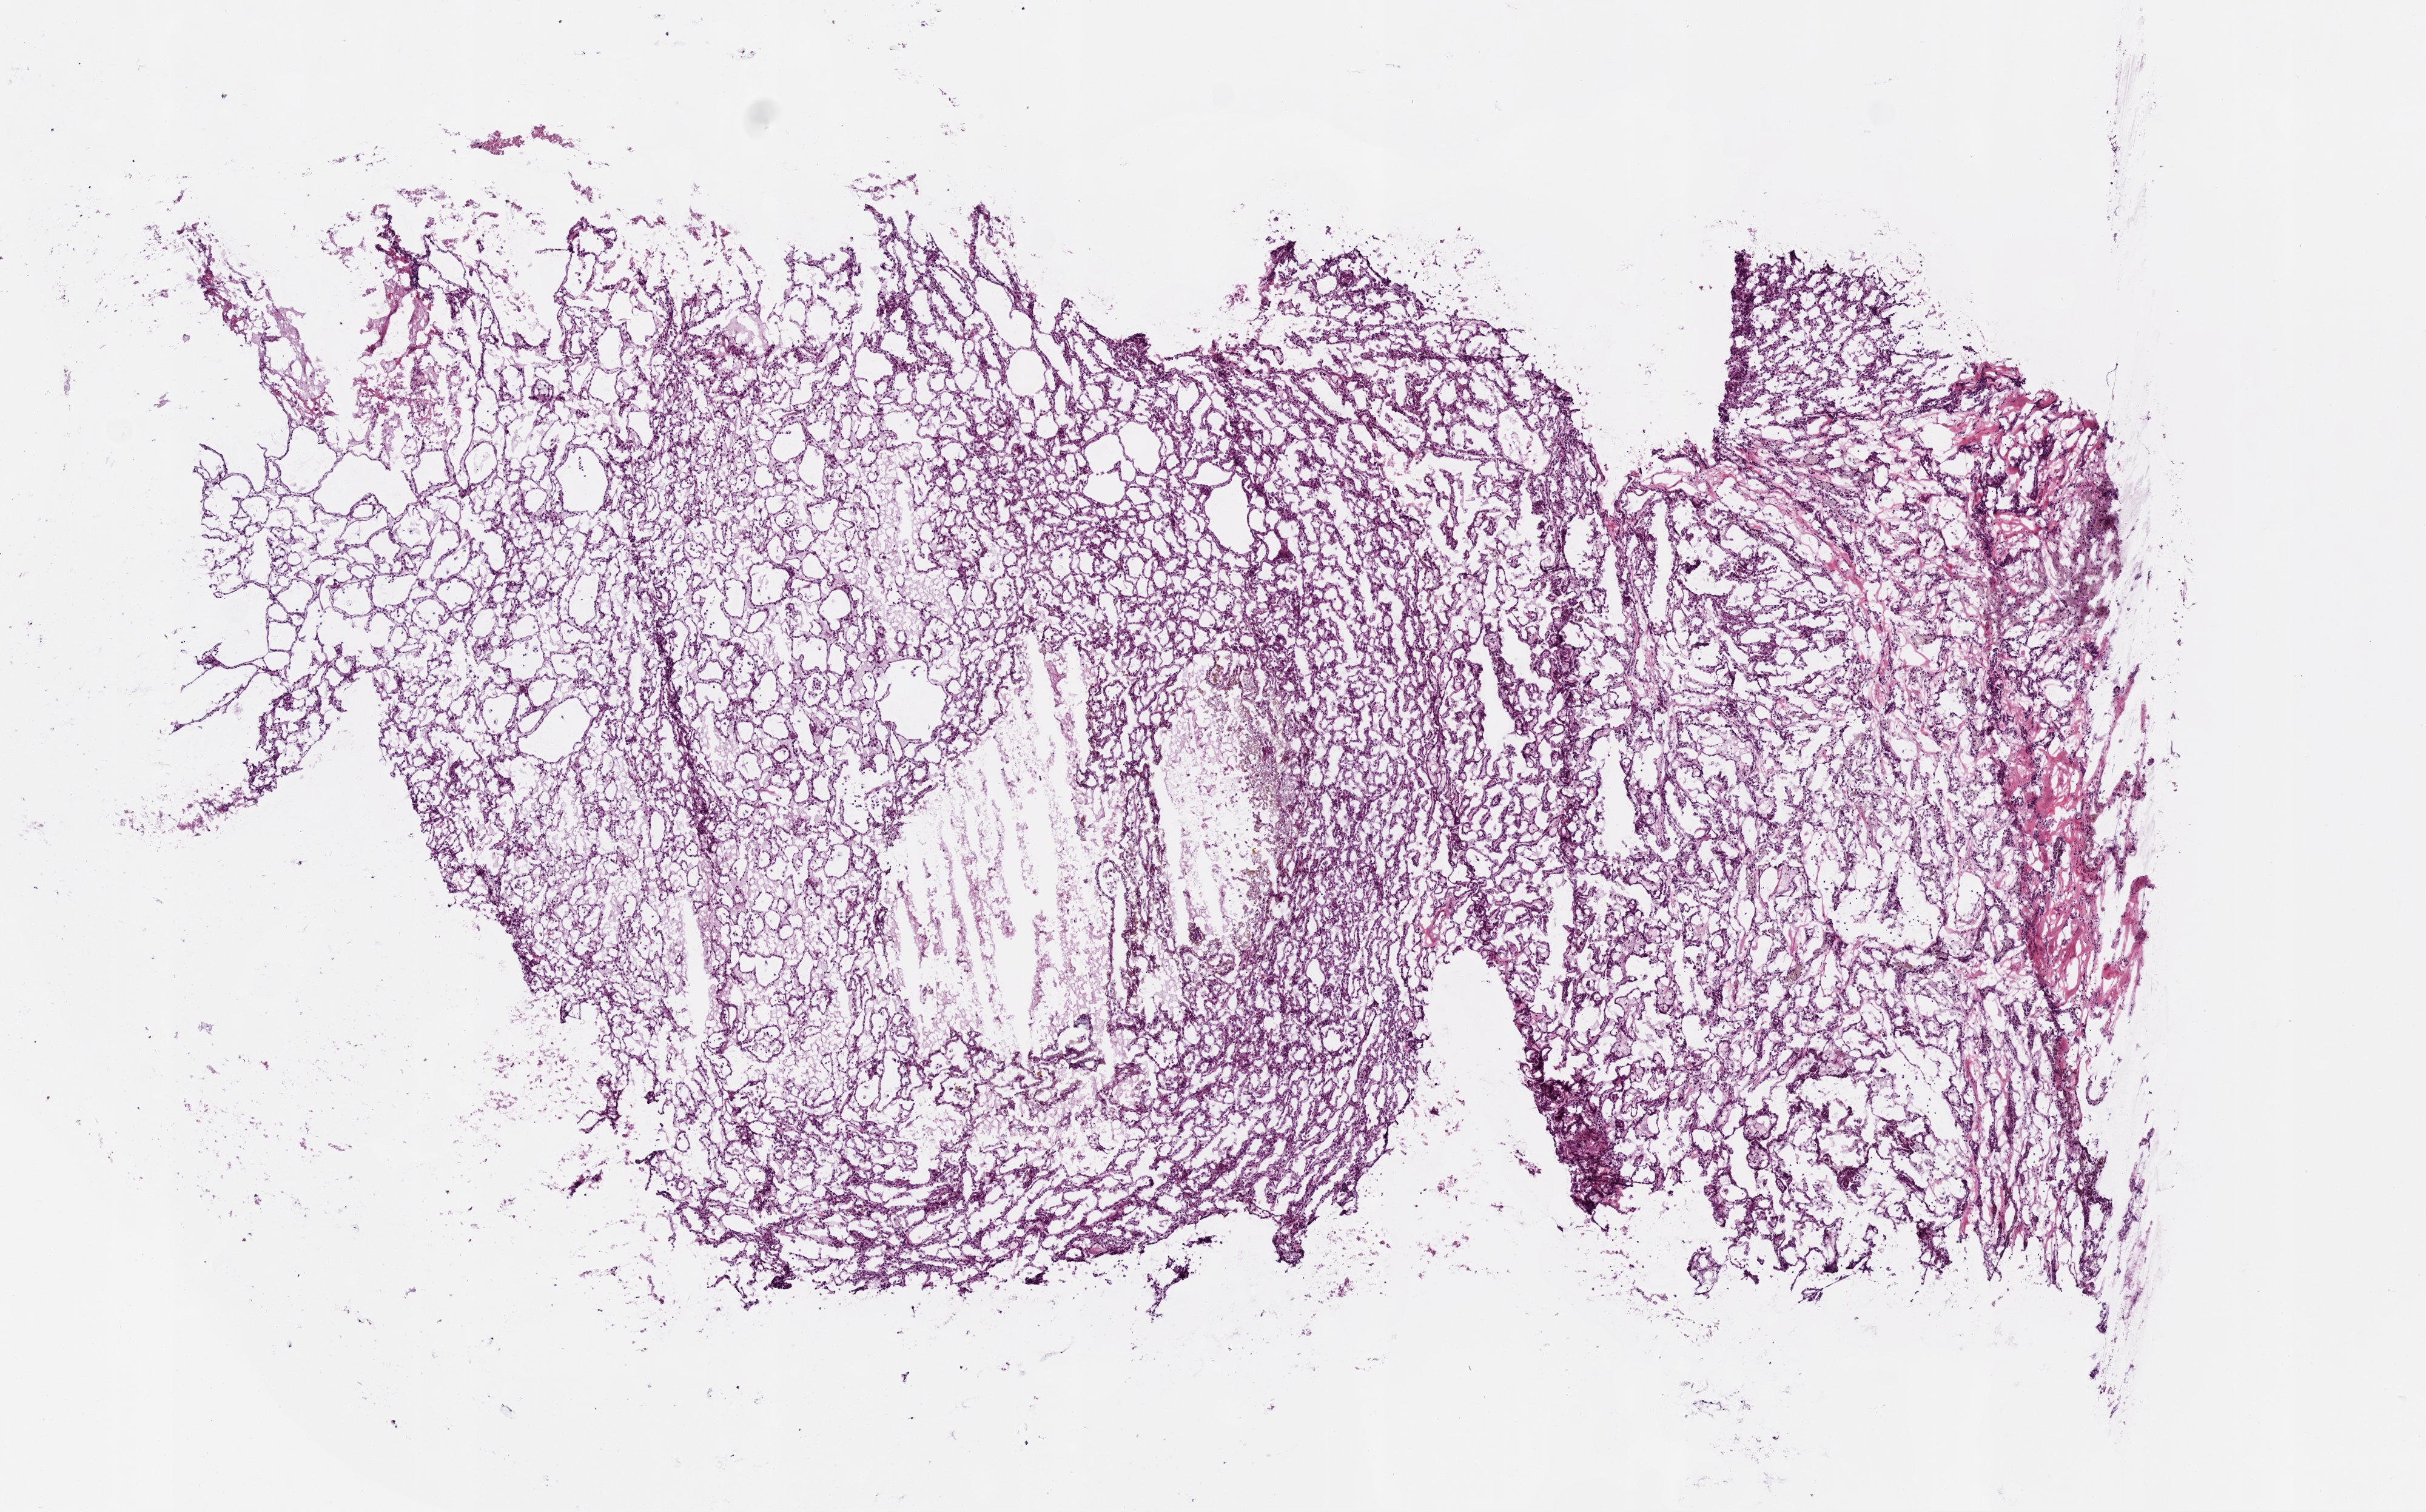
Whole-slide histology image, H&E, whole scanned area (about 8.0 x 5.0 mm, slide scanned at 20x) shown as a low-resolution overview, frozen section from the top of the tissue portion, primary tumour sample from the kidney. Patient: male, age at initial diagnosis 53 years. Composition of this section per pathologist review: tumour cells 90%, tumour nuclei 85%, normal cells 0%, stromal cells 10%, necrosis 0%.
Laterality: right. Pathologic diagnosis: Papillary adenocarcinoma, NOS. AJCC pathologic stage: I.